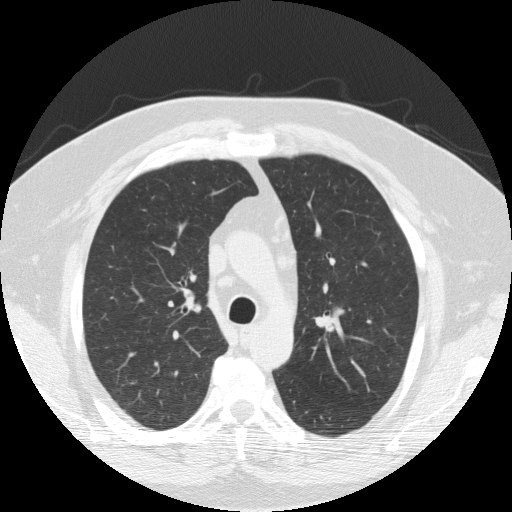
Axial slice from a low-dose chest CT screening exam, second annual screen, lung window (W 1500 / L -600 HU), standard (soft-tissue) reconstruction kernel (FC10), slice 75 of 227 in the series, 512 × 512 image matrix, field of view 379 × 379 mm. Male, age 60 years at enrolment. Current smoker at enrolment.
Expert-annotated lung lesion, bounding box <314,306,345,339> (left, top, right, bottom; pixels). Screening reader's record for this exam: no non-calcified nodule ≥4 mm recorded. Lung cancer was diagnosed 425 days after this screen (after the third annual screen): squamous cell carcinoma, NOS, right upper lobe, 27 mm at pathology.